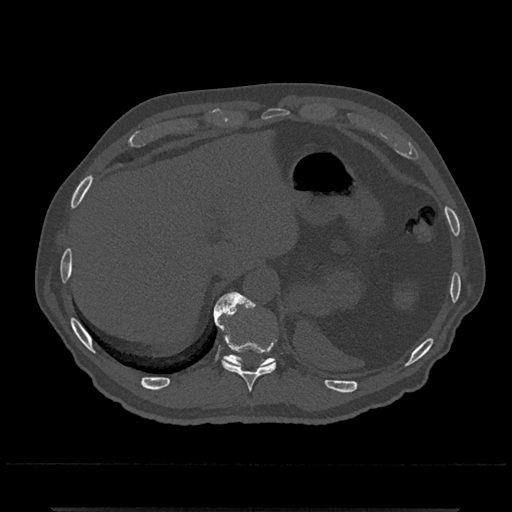
CT including the spine, one axial slice. Position 534 of 797 along the scan axis. Reconstruction kernel Br40s/3. Bone window (W 1800 / L 400 HU). 512 × 512 image matrix. Patient: male, 67 years. From the clinical record (not read from this slice): primary cancer: prostate.
Structures marked on this image (semi-automatically segmented with operator editing):
- T10 vertebra: bounding box [x1, y1, x2, y2] px = [214, 292, 276, 392]
- T11 vertebra: [213, 293, 276, 367]